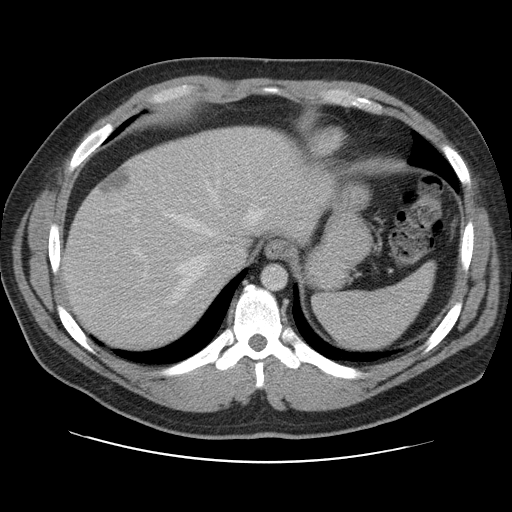
Contrast-enhanced abdominal CT, one axial slice; slice 89 of 109 in the series (ordered by position); soft-tissue window (W 400 / L 40 HU); 5 mm slice thickness; 512 × 512 image matrix, field of view 402 × 402 mm. Male patient, age 35 years. Case-level facts recorded for this patient, not image findings: diagnosis: colorectal cancer liver metastases, imaged before liver resection; multiple liver metastases: yes; largest metastasis: 2.8 cm; chemotherapy before resection: yes.
Outlined on this slice (outlined manually by an expert reader):
- hepatic veins: bounding box <140,180,267,318> (left, top, right, bottom; pixels)
- liver: <63,127,326,352>
- planned liver remnant (the part of the liver to remain after resection): <64,126,327,351>
- portal vein (with intrahepatic branches): <128,165,183,280>
- liver metastasis: <102,170,130,195>